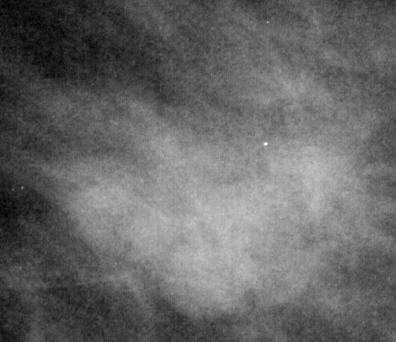
Region of interest cut from a scanned film mammogram (one marked finding); right breast; MLO view.
Marked abnormality: mass, shape lobulated, margins spiculated; BI-RADS assessment category 5; pathology (as recorded): malignant.